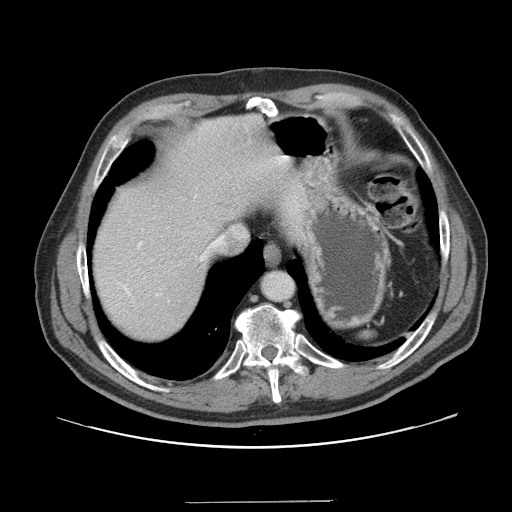
Contrast-enhanced abdominal CT, one axial slice. Slice 134 of 151 in the series (ordered by position). 120 kVp. Intravenous contrast given. Soft-tissue window (W 400 / L 40 HU). 2.5 mm slice thickness. 512 × 512 image matrix. Male patient, age 63 years. Case-level facts recorded for this patient, not image findings: diagnosis: colorectal cancer liver metastases, imaged before liver resection; multiple liver metastases: no; largest metastasis: 2.1 cm; disease in both lobes: no.
Annotated regions visible in this slice (manually delineated by an expert):
- hepatic veins: box from (x=202, y=237) to (x=223, y=259) px
- liver: (x=92, y=115)–(x=303, y=344)
- planned liver remnant (the part of the liver to remain after resection): (x=92, y=134)–(x=239, y=344)